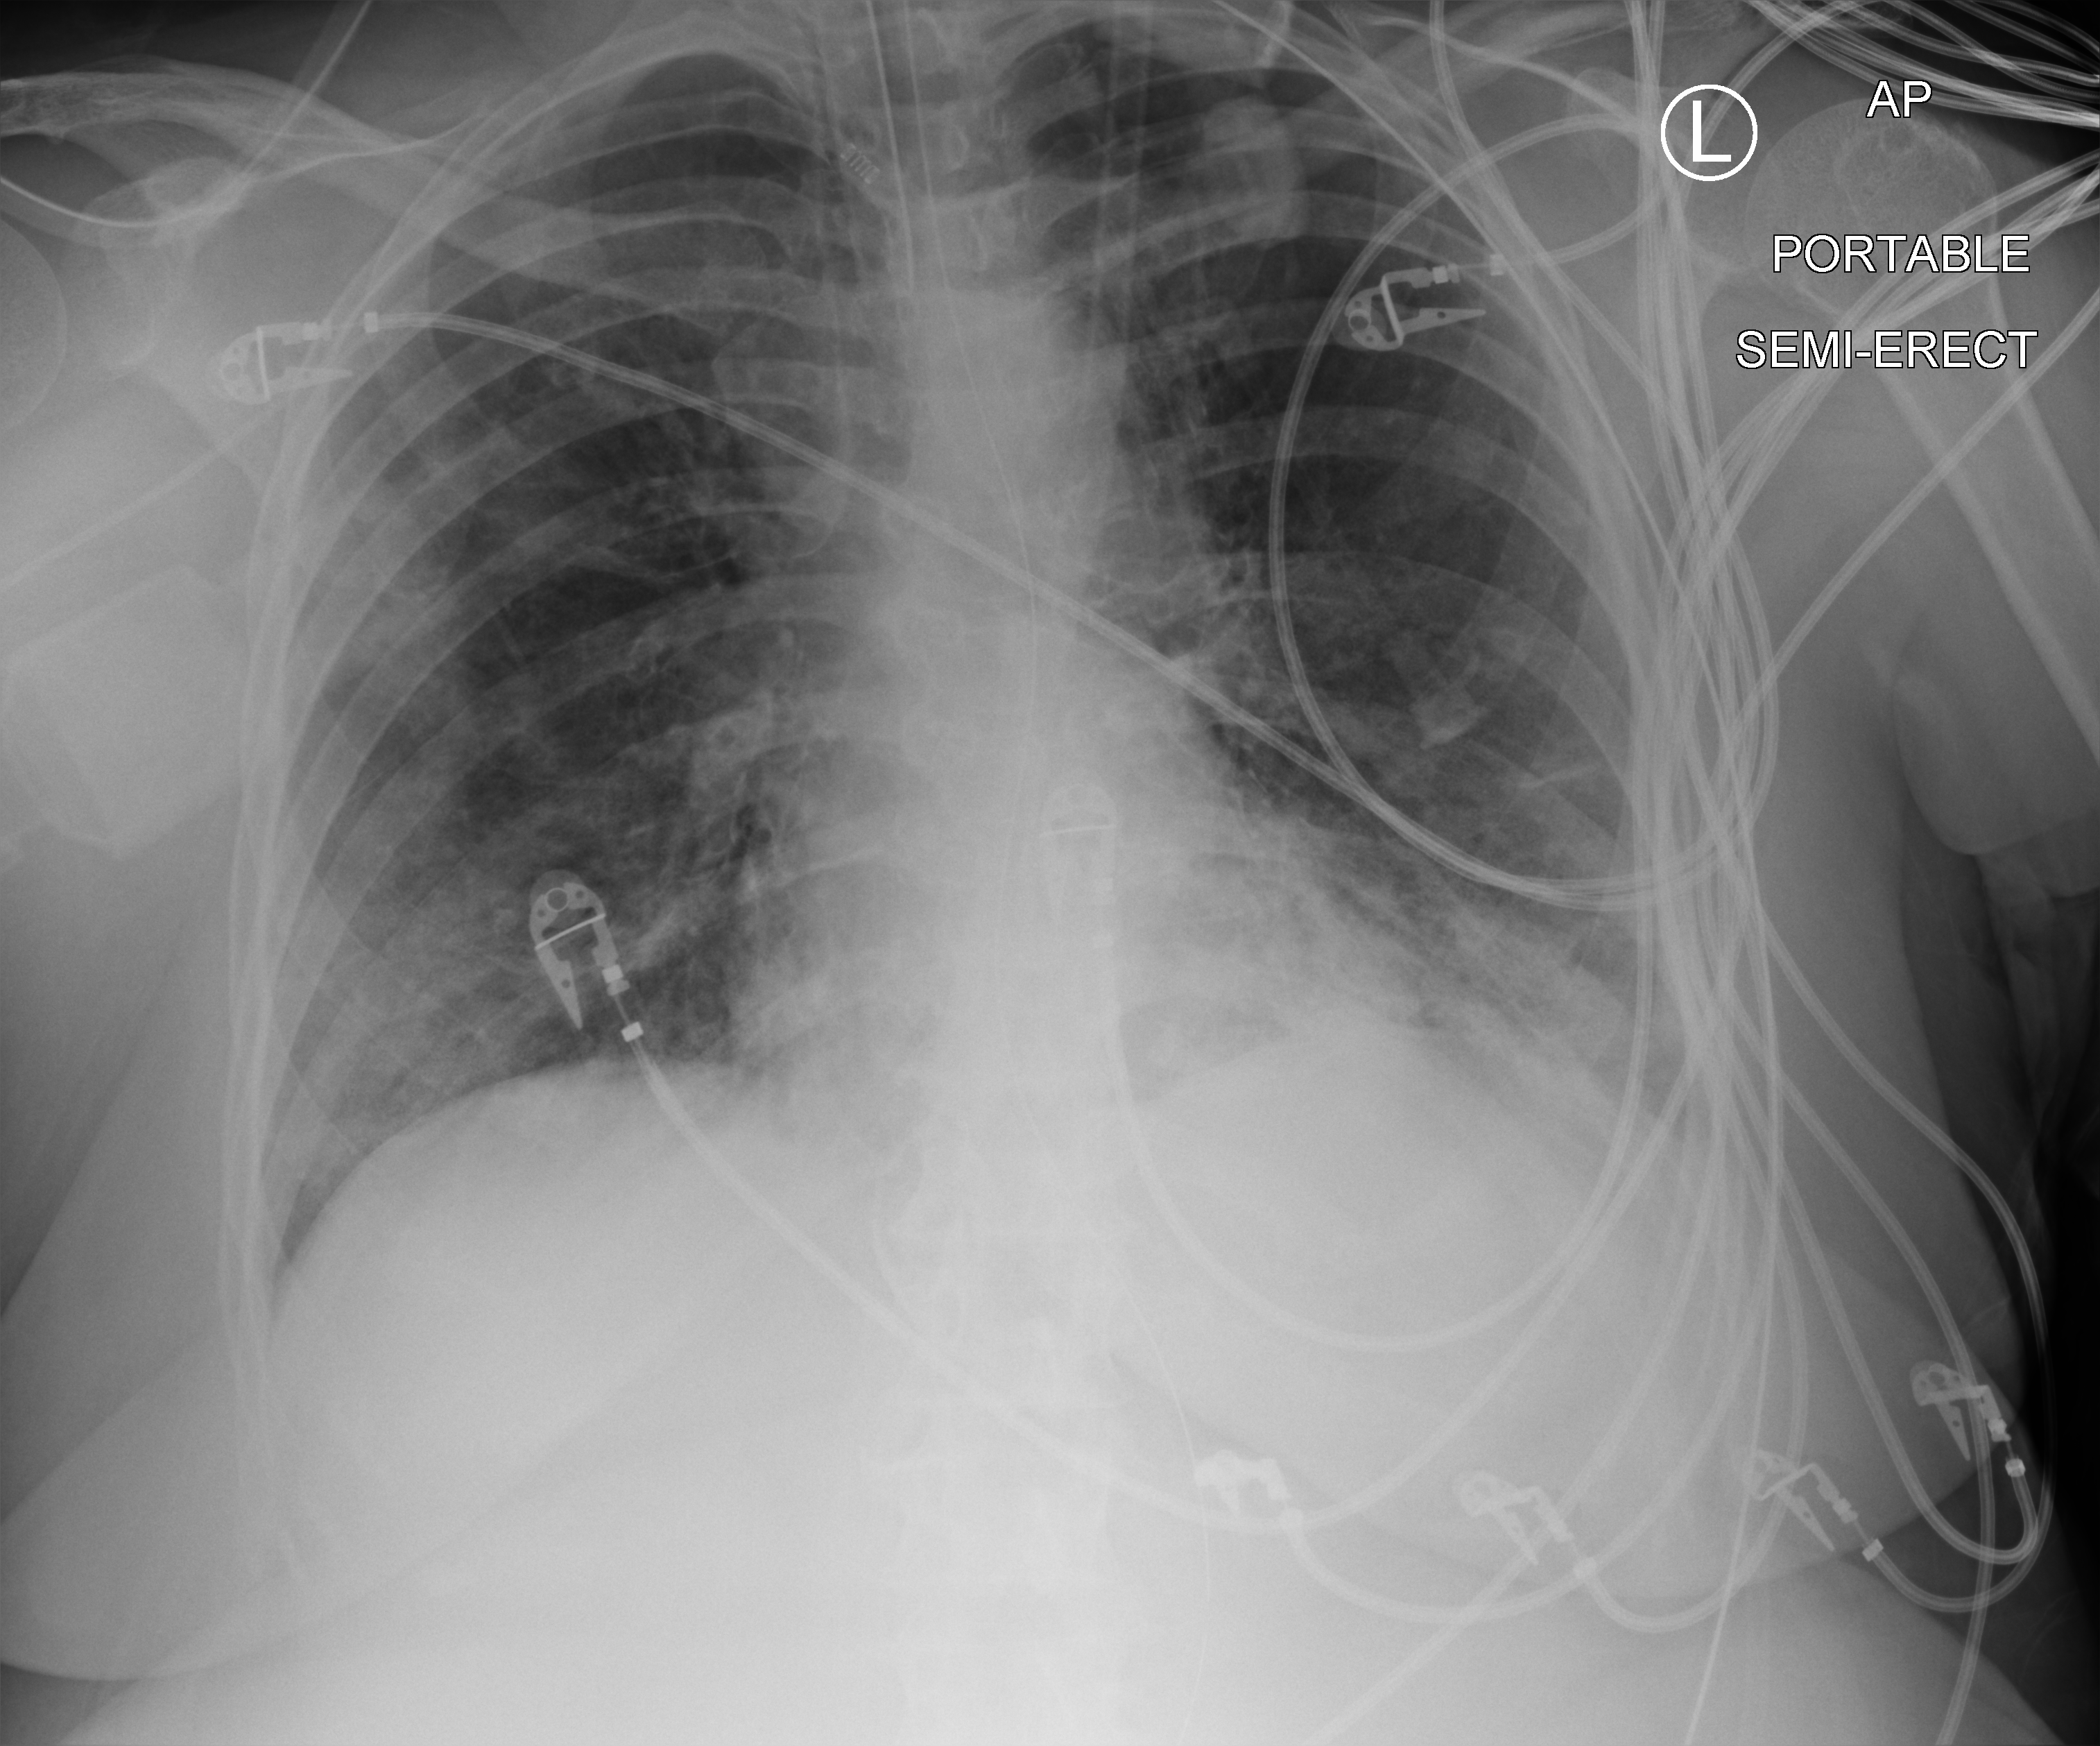
Portable chest radiograph; anteroposterior (AP) projection. Female patient hospitalised with COVID-19, age 75–90 years.
Hospital-stay facts (about this admission, not read from this image; timing relative to this image not recorded): chronic kidney disease (admission record): no.